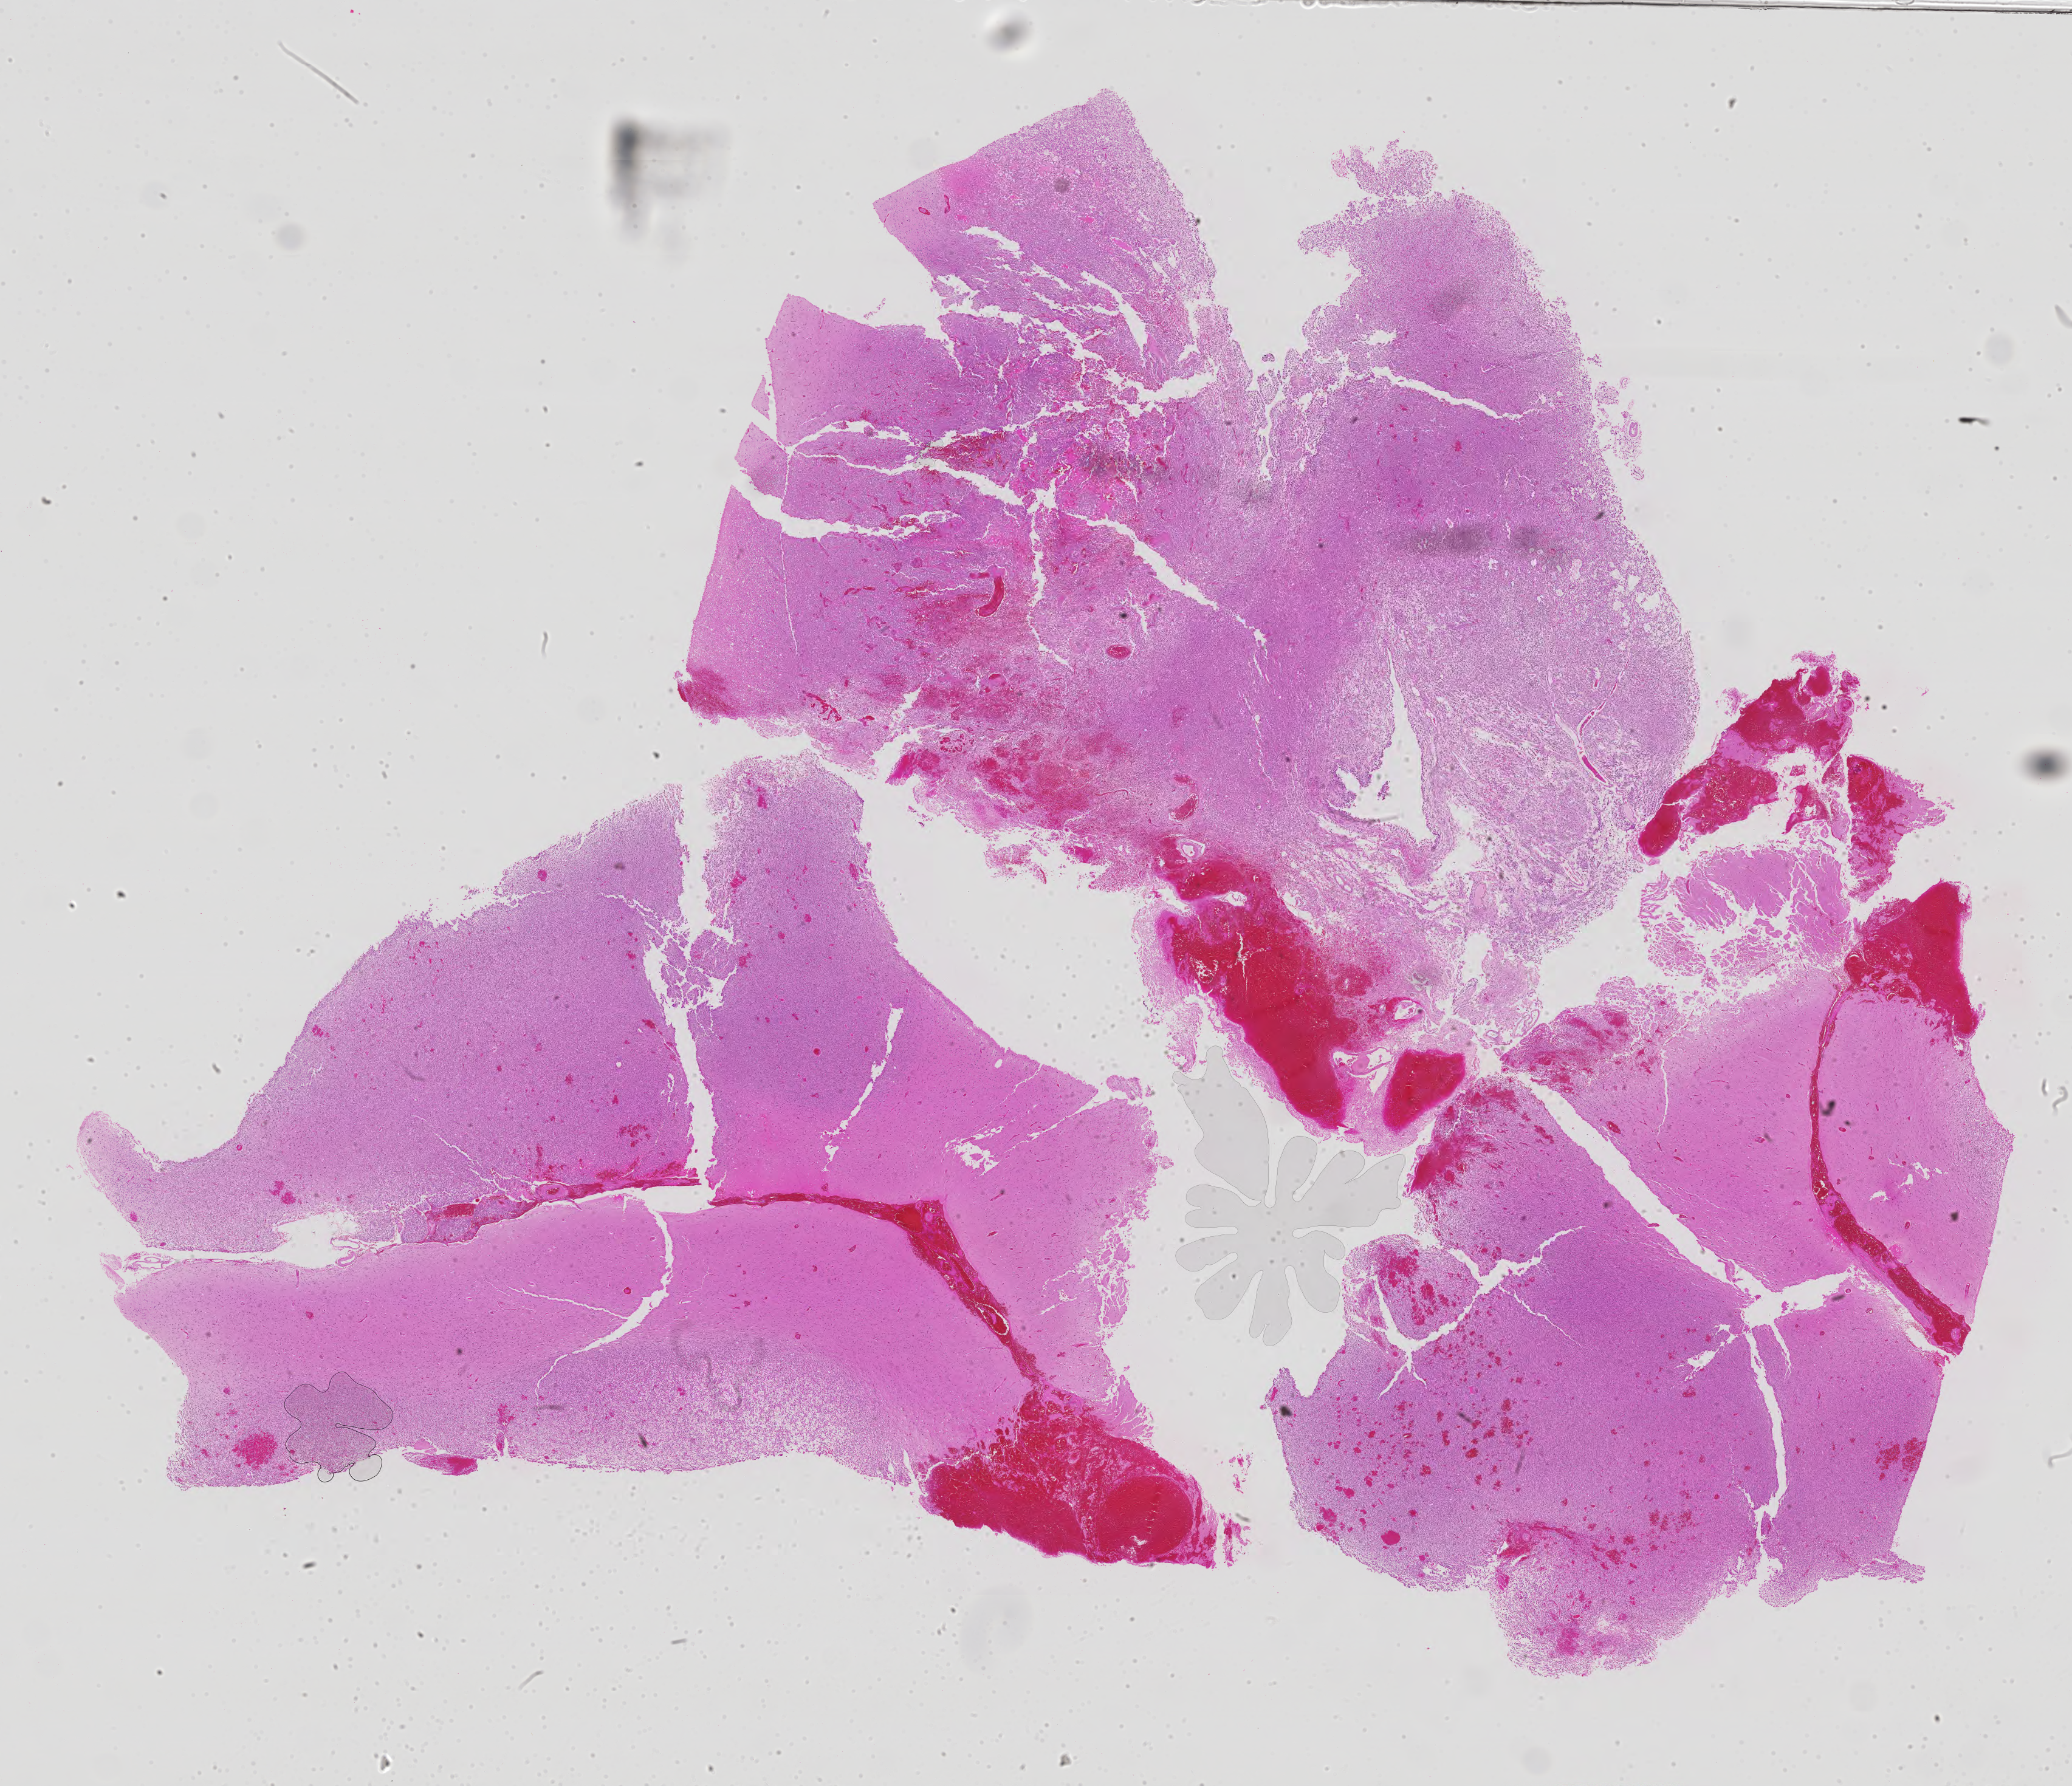
Digitized H&E tissue section (whole slide) — low-resolution overview of the scanned area, about 27.3 x 23.5 mm (from a 40x scan). FFPE section. Sample: primary tumour, brain. Patient: male, age at initial diagnosis 71 years. Histologic grade: G3 (poorly differentiated).
Diagnosis: Oligodendroglioma, anaplastic (cerebrum).